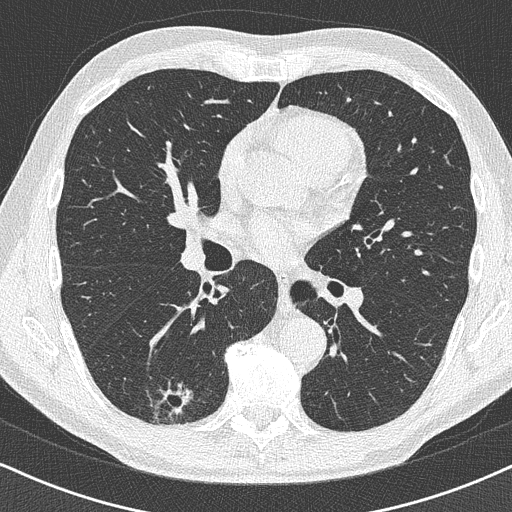
Axial slice from a low-dose chest CT screening exam, baseline annual screen, lung window (W 1500 / L -600 HU), 1 mm slice thickness, 120 kVp, slice 208 of 438 in the series. Male participant, aged 63 years at enrolment.
• Expert-annotated lung lesion, box from (x=138, y=373) to (x=209, y=431) px.
• Screening reader's record for this exam (one nodule recorded; not confirmed to be the boxed lesion): non-calcified nodule or mass ≥4 mm, right lower lobe, 16 × 13 mm, poorly defined margins.